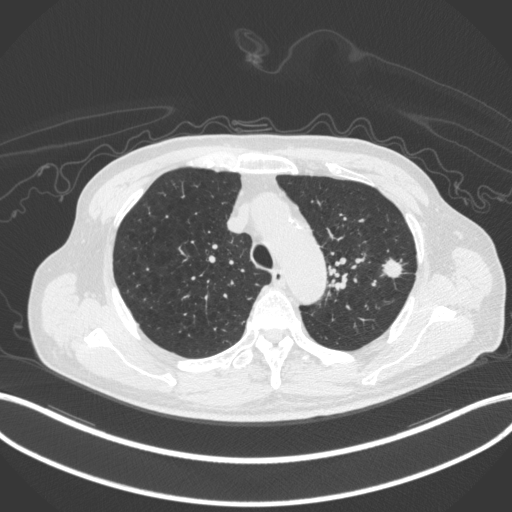
Chest CT, one axial slice; position 337 of 420 along the scan axis; reconstruction kernel B31f; 120 kVp; lung window (W 1500 / L -600 HU); 512 × 512 image matrix, field of view 400 × 400 mm. Male patient, age 77 years. From the clinical record (not read from this slice): clinical TNM (as recorded): T3 N1 M0.
Outlined on this slice (bounding box drawn by a radiologist):
- lung tumour (recorded histology: adenocarcinoma): bounding box (x1, y1, x2, y2) in pixels: (378, 256, 403, 280)